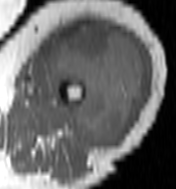
MRI of an extremity soft-tissue mass, one axial slice; slice 57 of 100 in the series (ordered by position); MR volume resampled by the dataset authors to the PET/CT grid (not the native acquisition matrix); 3.27 mm slice thickness; 176 × 189 image matrix, field of view 172 × 185 mm. Female patient. Case-level facts recorded for this patient, not image findings: histological type: undifferentiated – high grade; grade: high; site of the primary tumour: left thigh.
Structures marked on this image (expert contour drawn on MRI and transferred to this co-registered scan by the dataset authors):
- gross tumour volume including surrounding oedema: bounding box [x1, y1, x2, y2] px = [46, 25, 145, 149]
- gross tumour volume (mass): [46, 25, 145, 149]